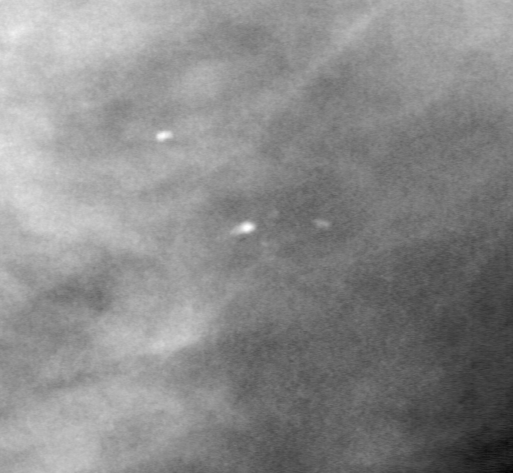
Region of interest cut from a scanned film mammogram (one marked finding), right breast, MLO view.
- Marked abnormality: calcifications, morphology pleomorphic, distribution clustered; BI-RADS assessment category 4; pathology (as recorded): benign.